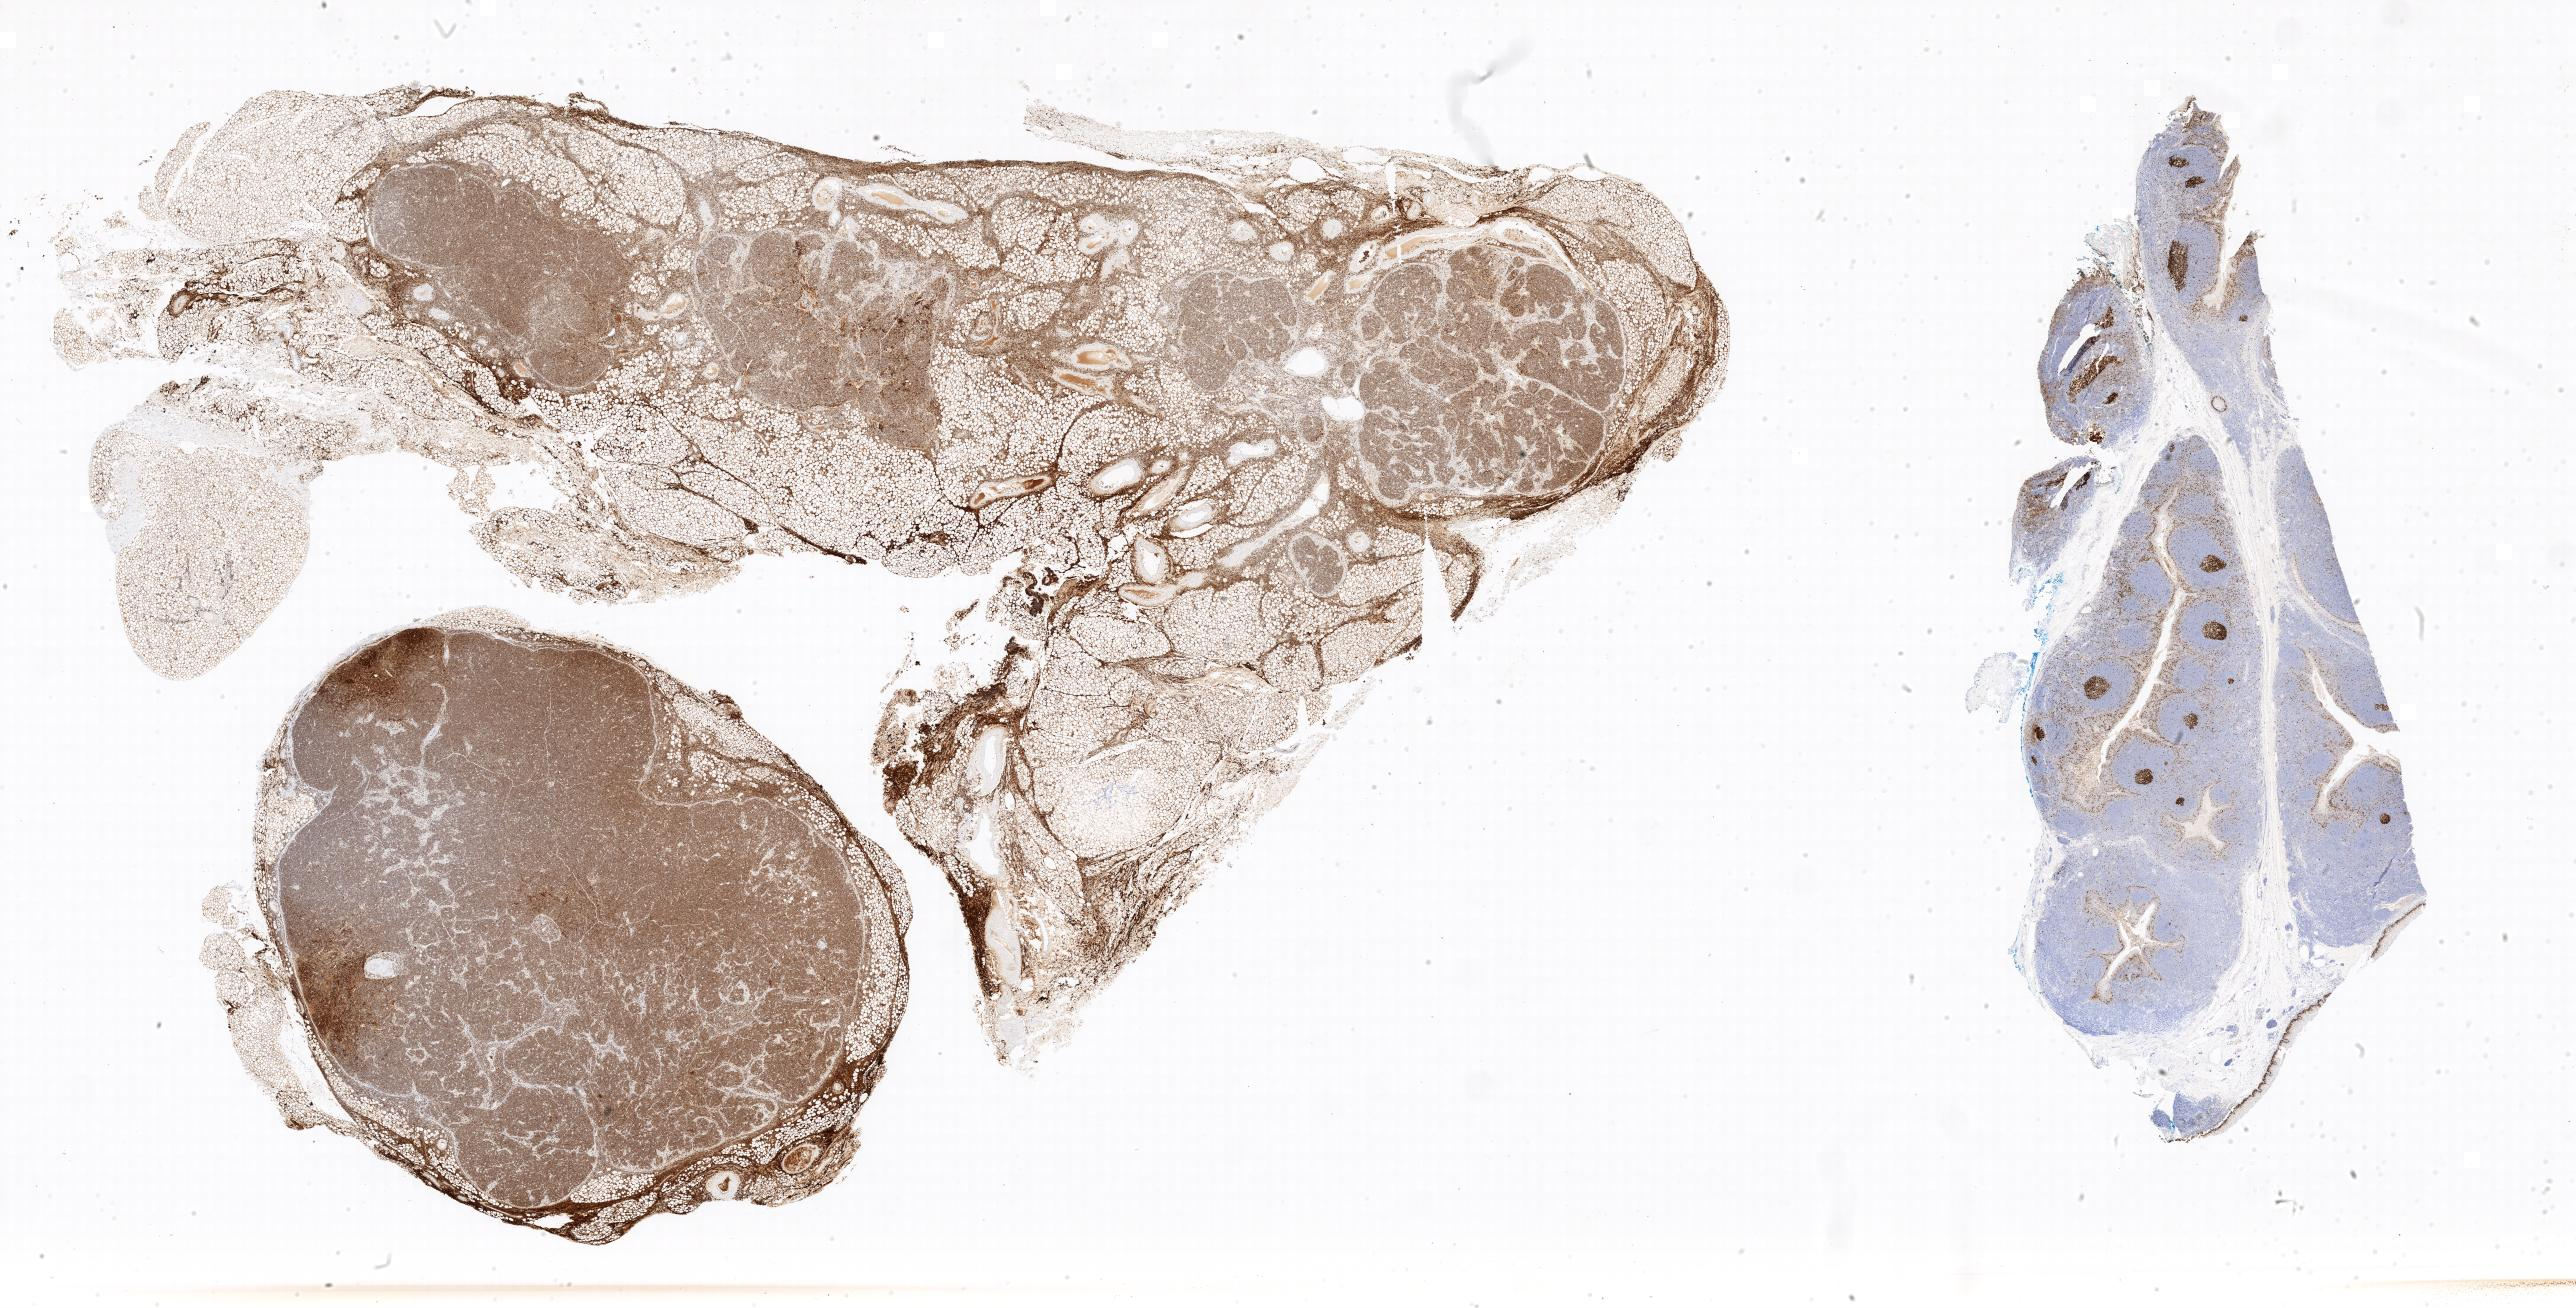
IHC for Ki-67, whole-slide image — shown as a low-resolution overview of the whole scanned area. Tumor tissue. Anatomic site: spleen. Female patient, 15 years old.
• diagnosis: Burkitt lymphoma, NOS